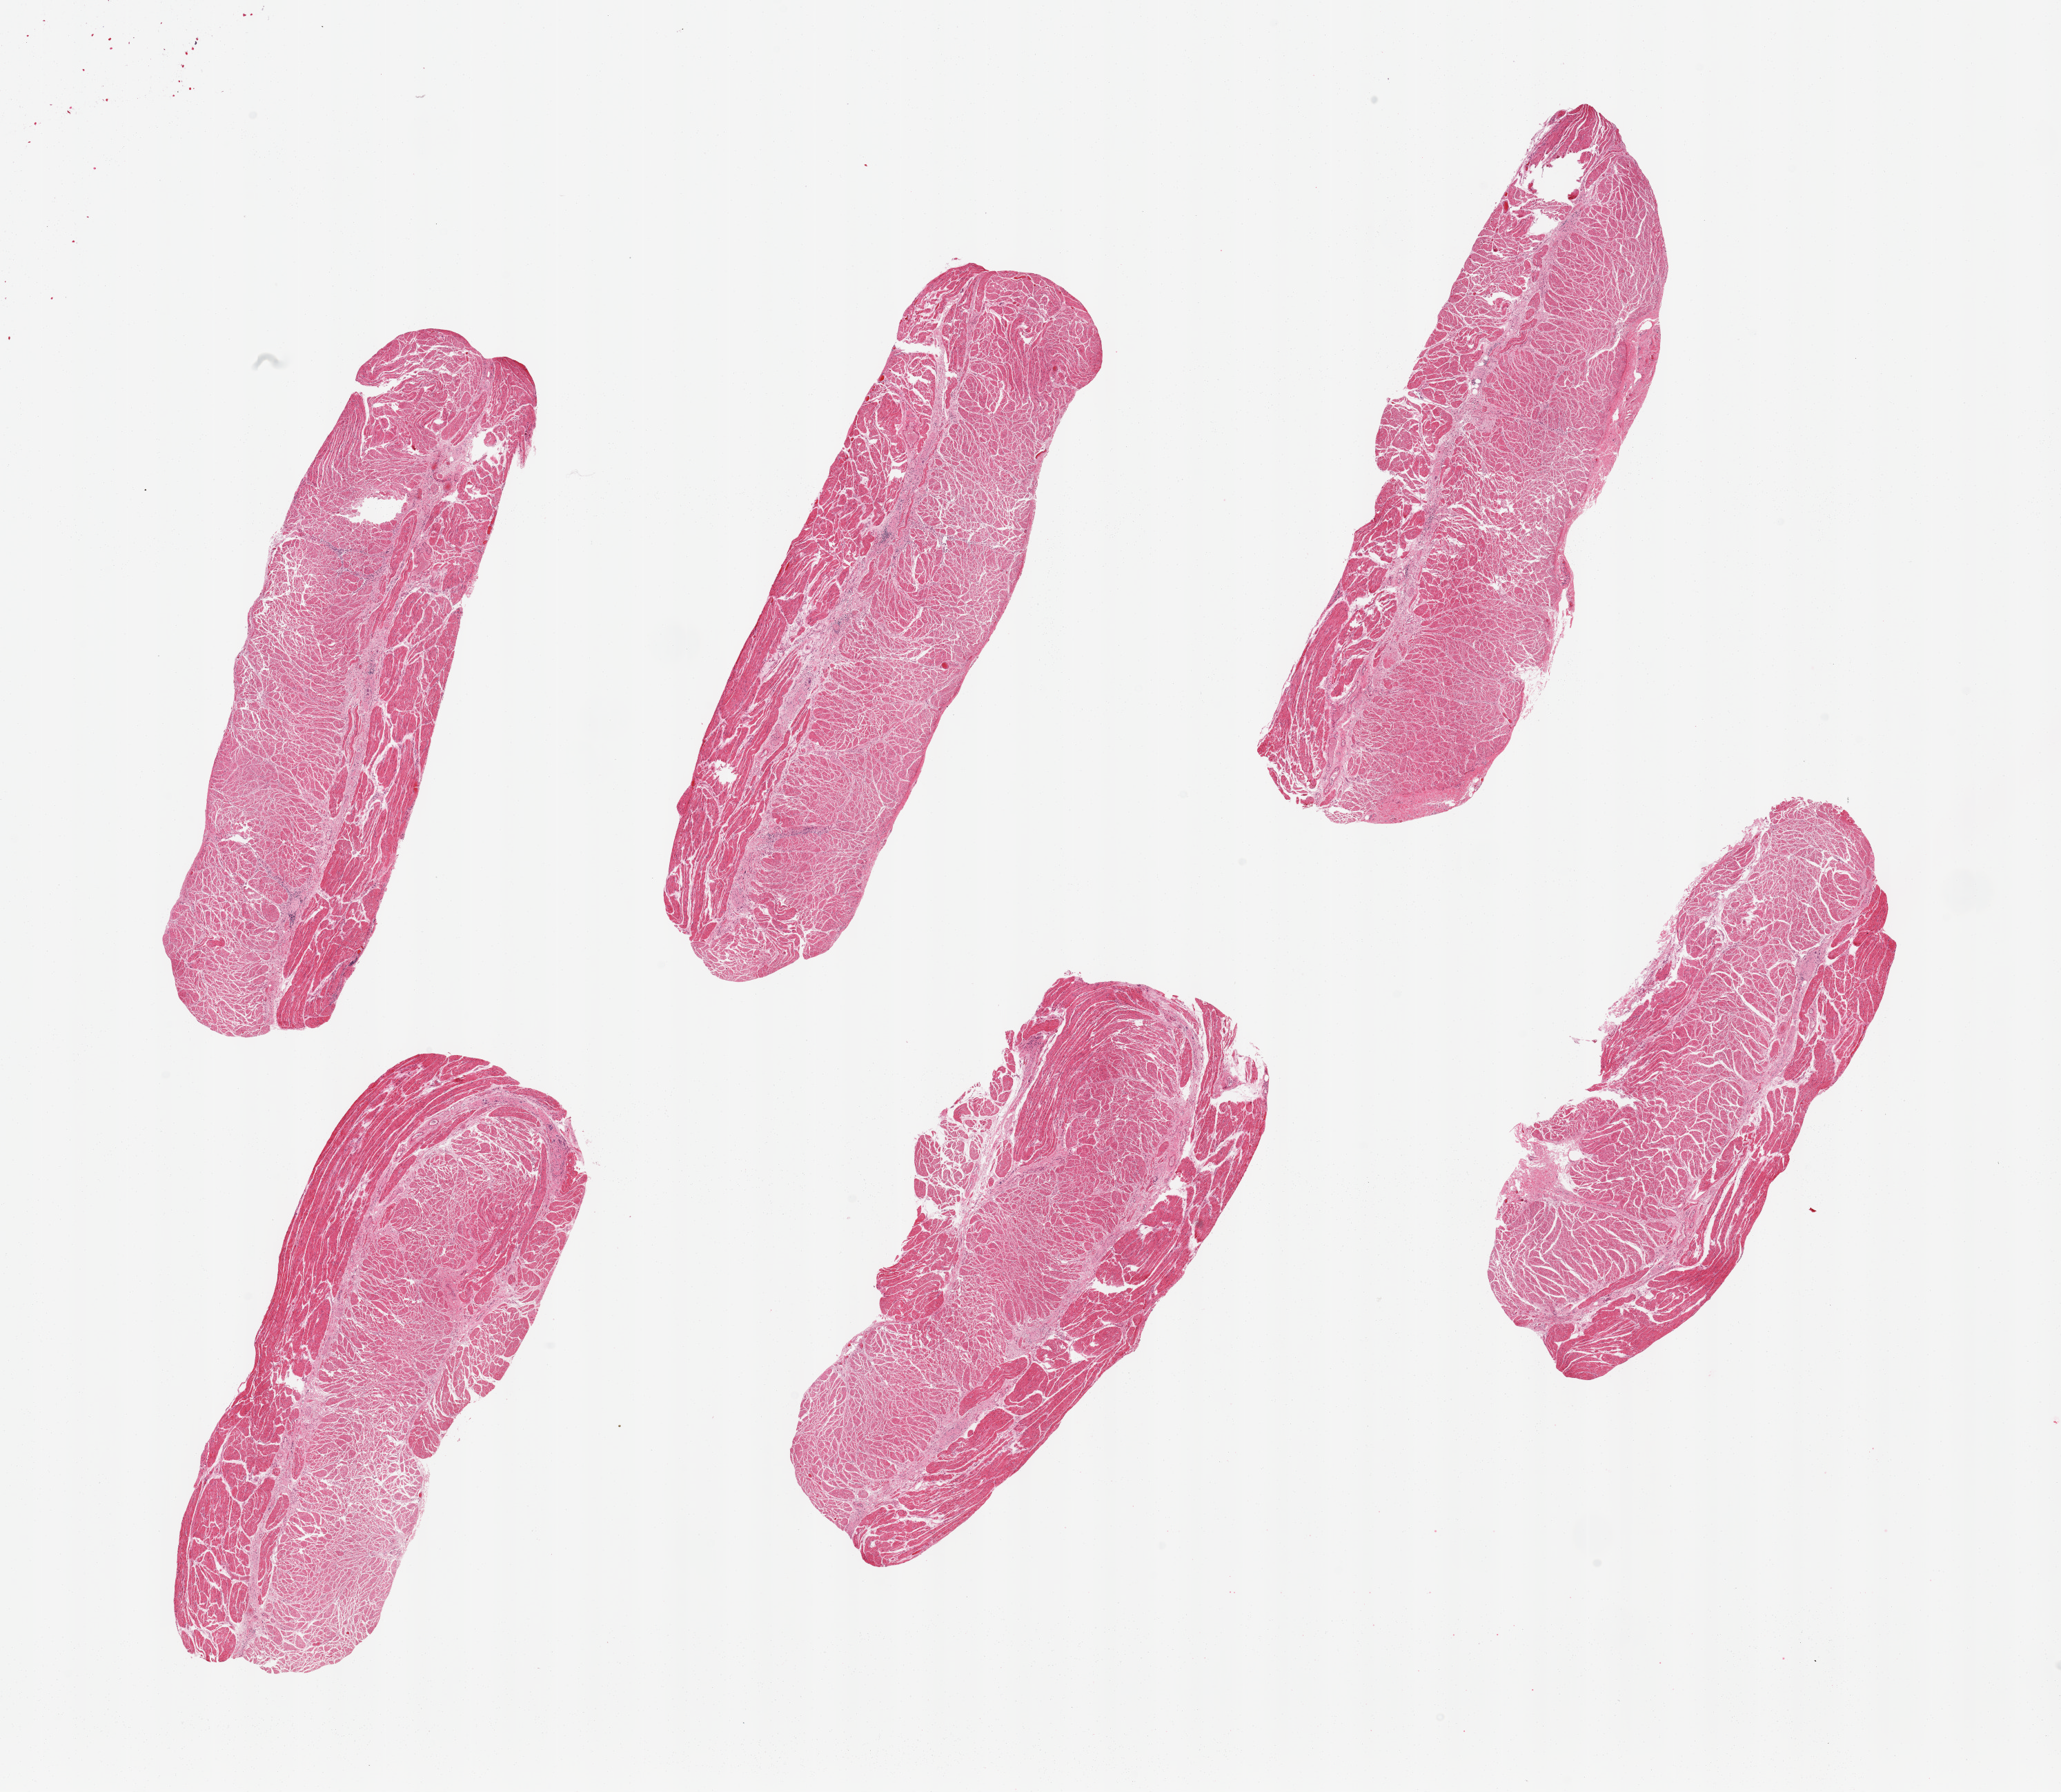
H&E whole-slide image, low-resolution overview of the scanned area, about 23.6 x 20.5 mm; PAXgene-fixed, paraffin-embedded tissue; section of gastroesophageal junction (target tissue); tissue donor sample. Donor sex: male.
Review note (as recorded): 6 pieces, confirmed target muscularis.